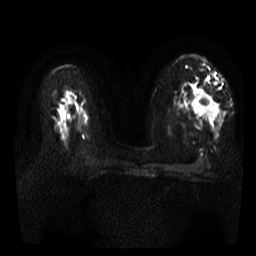
Breast MRI, one axial slice; position 18 of 35 along the scan axis; diffusion-weighted series; image 2 of 4 stored at this slice position (different b-values; order by instance number); 3 T; 256 × 256 image matrix, field of view 300 × 300 mm. Female patient.
Outlined on this slice (manually delineated by an expert):
- tumour on diffusion-weighted imaging: bounding box [x1, y1, x2, y2] px = [192, 94, 217, 118]